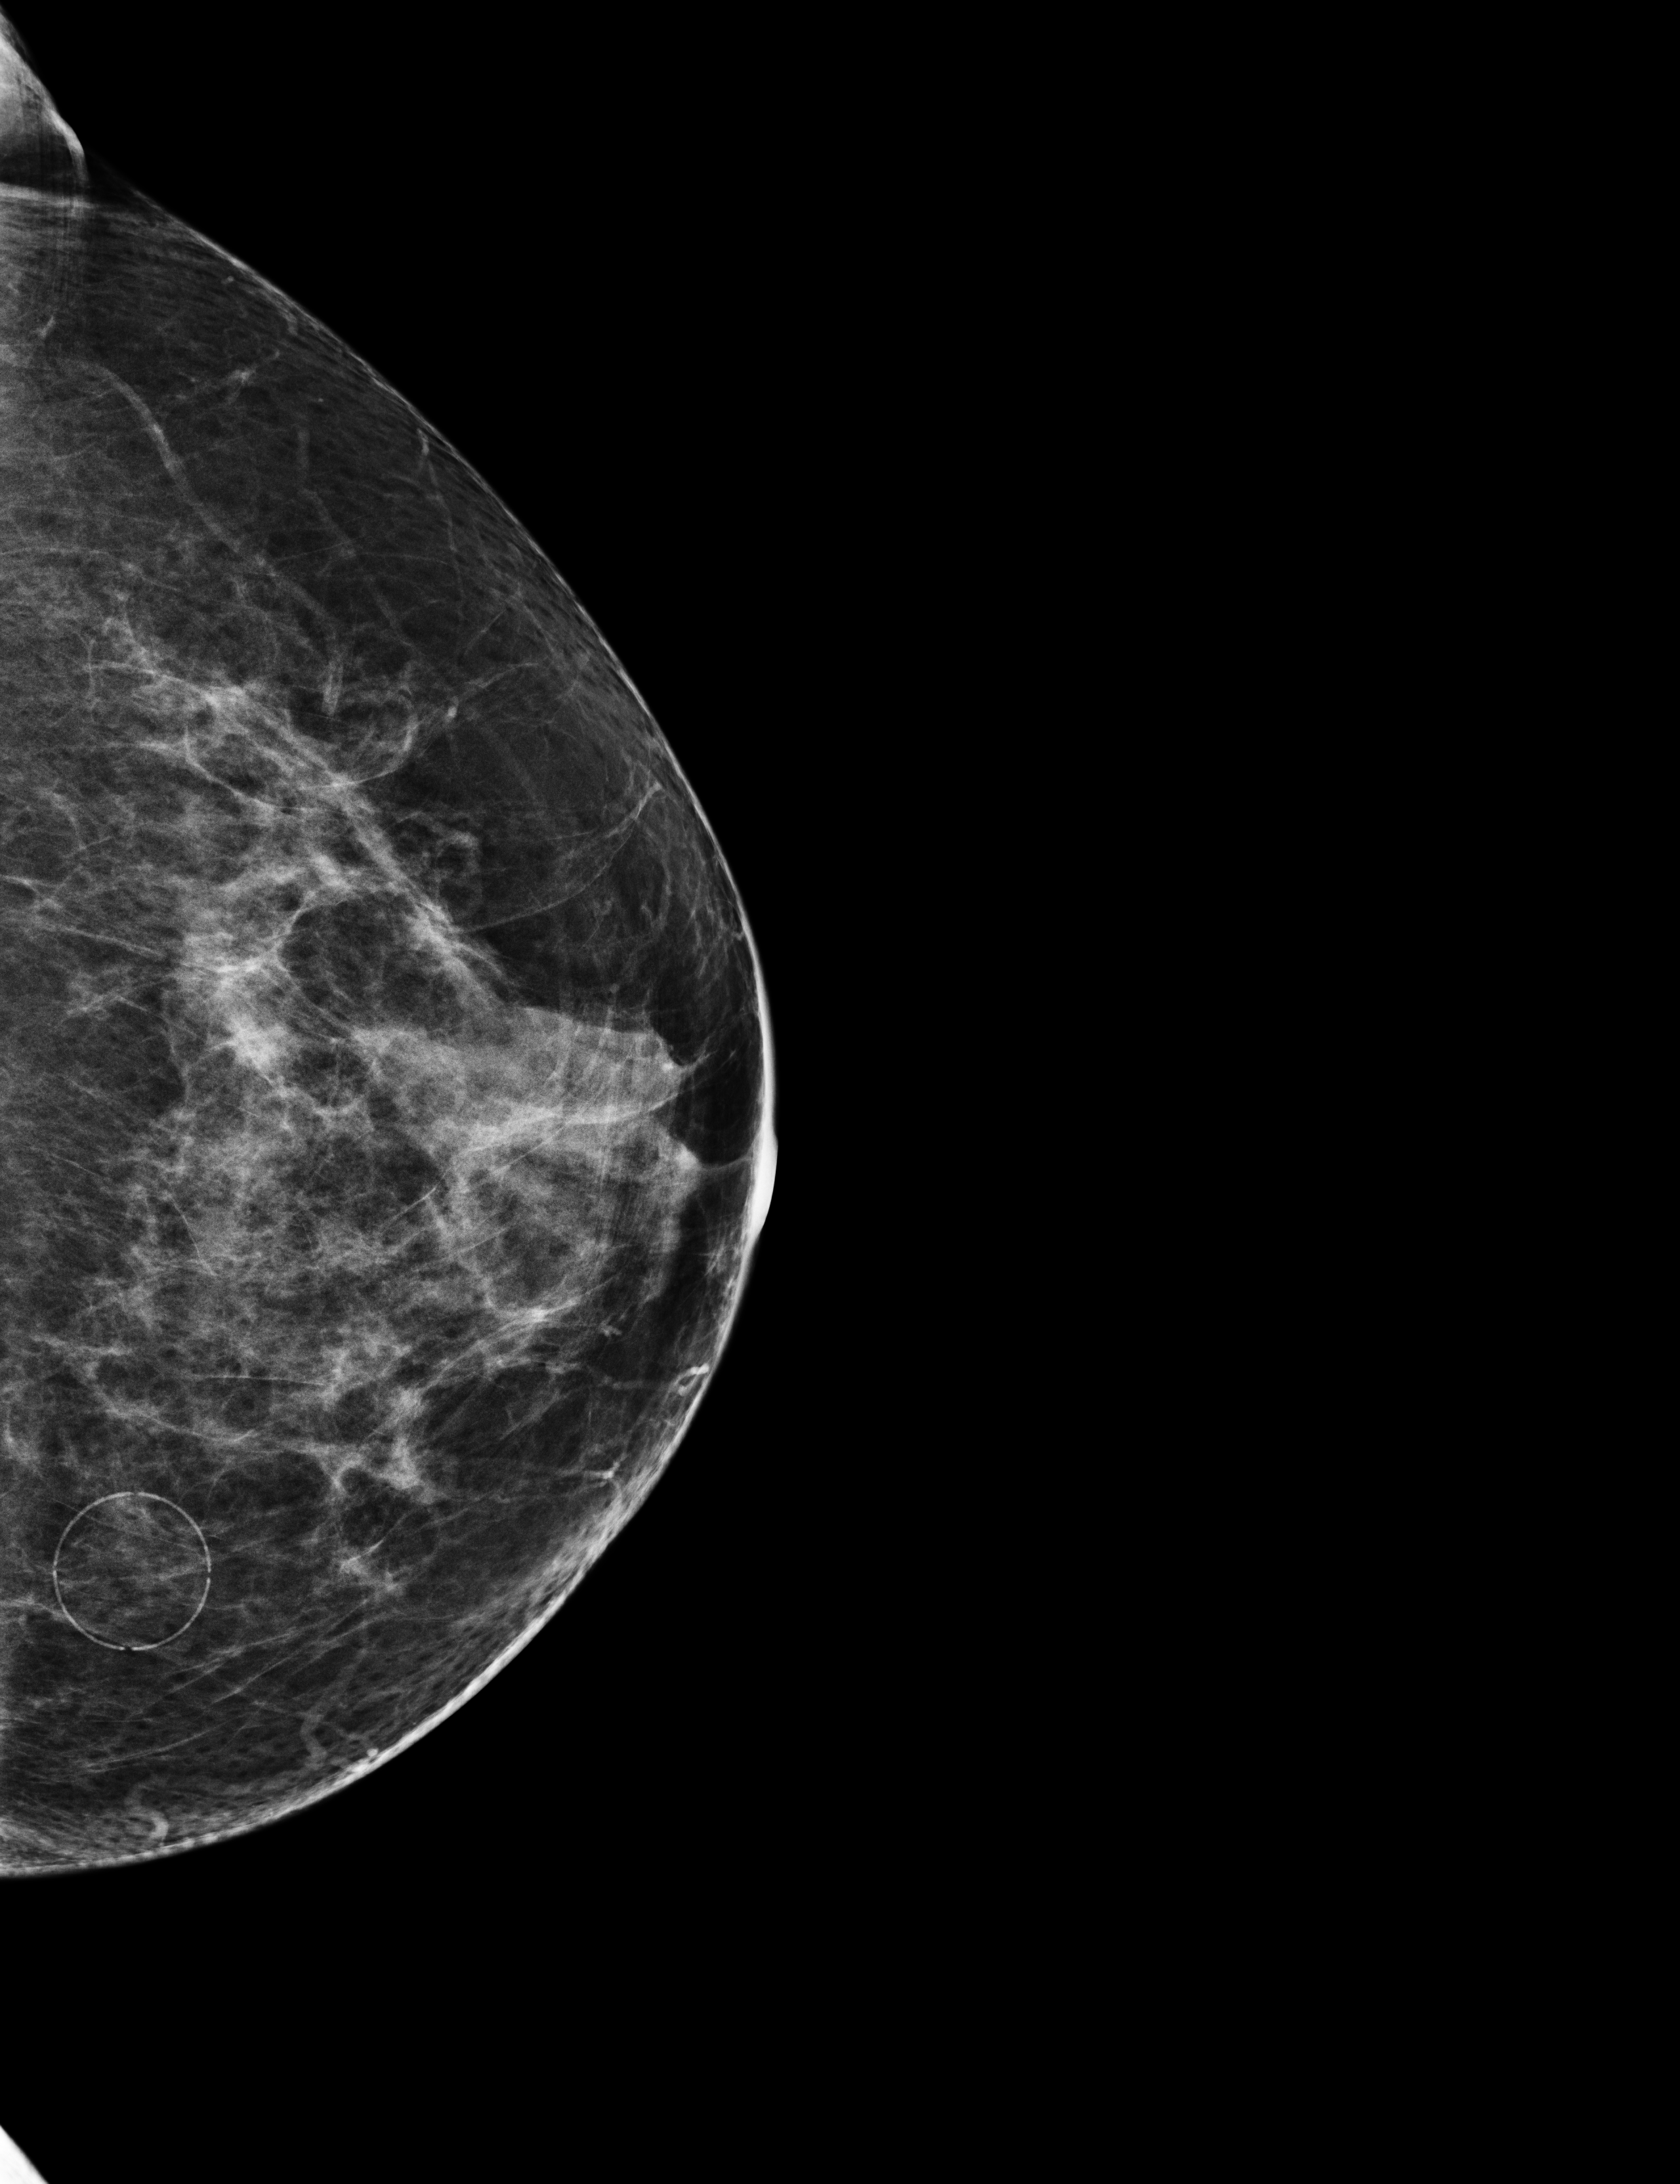
Screening examination; compressed breast thickness 55 mm. Patient: female, 61 years.
Image type: full-field digital mammogram. Breast: left. Projection: craniocaudal (CC) view.